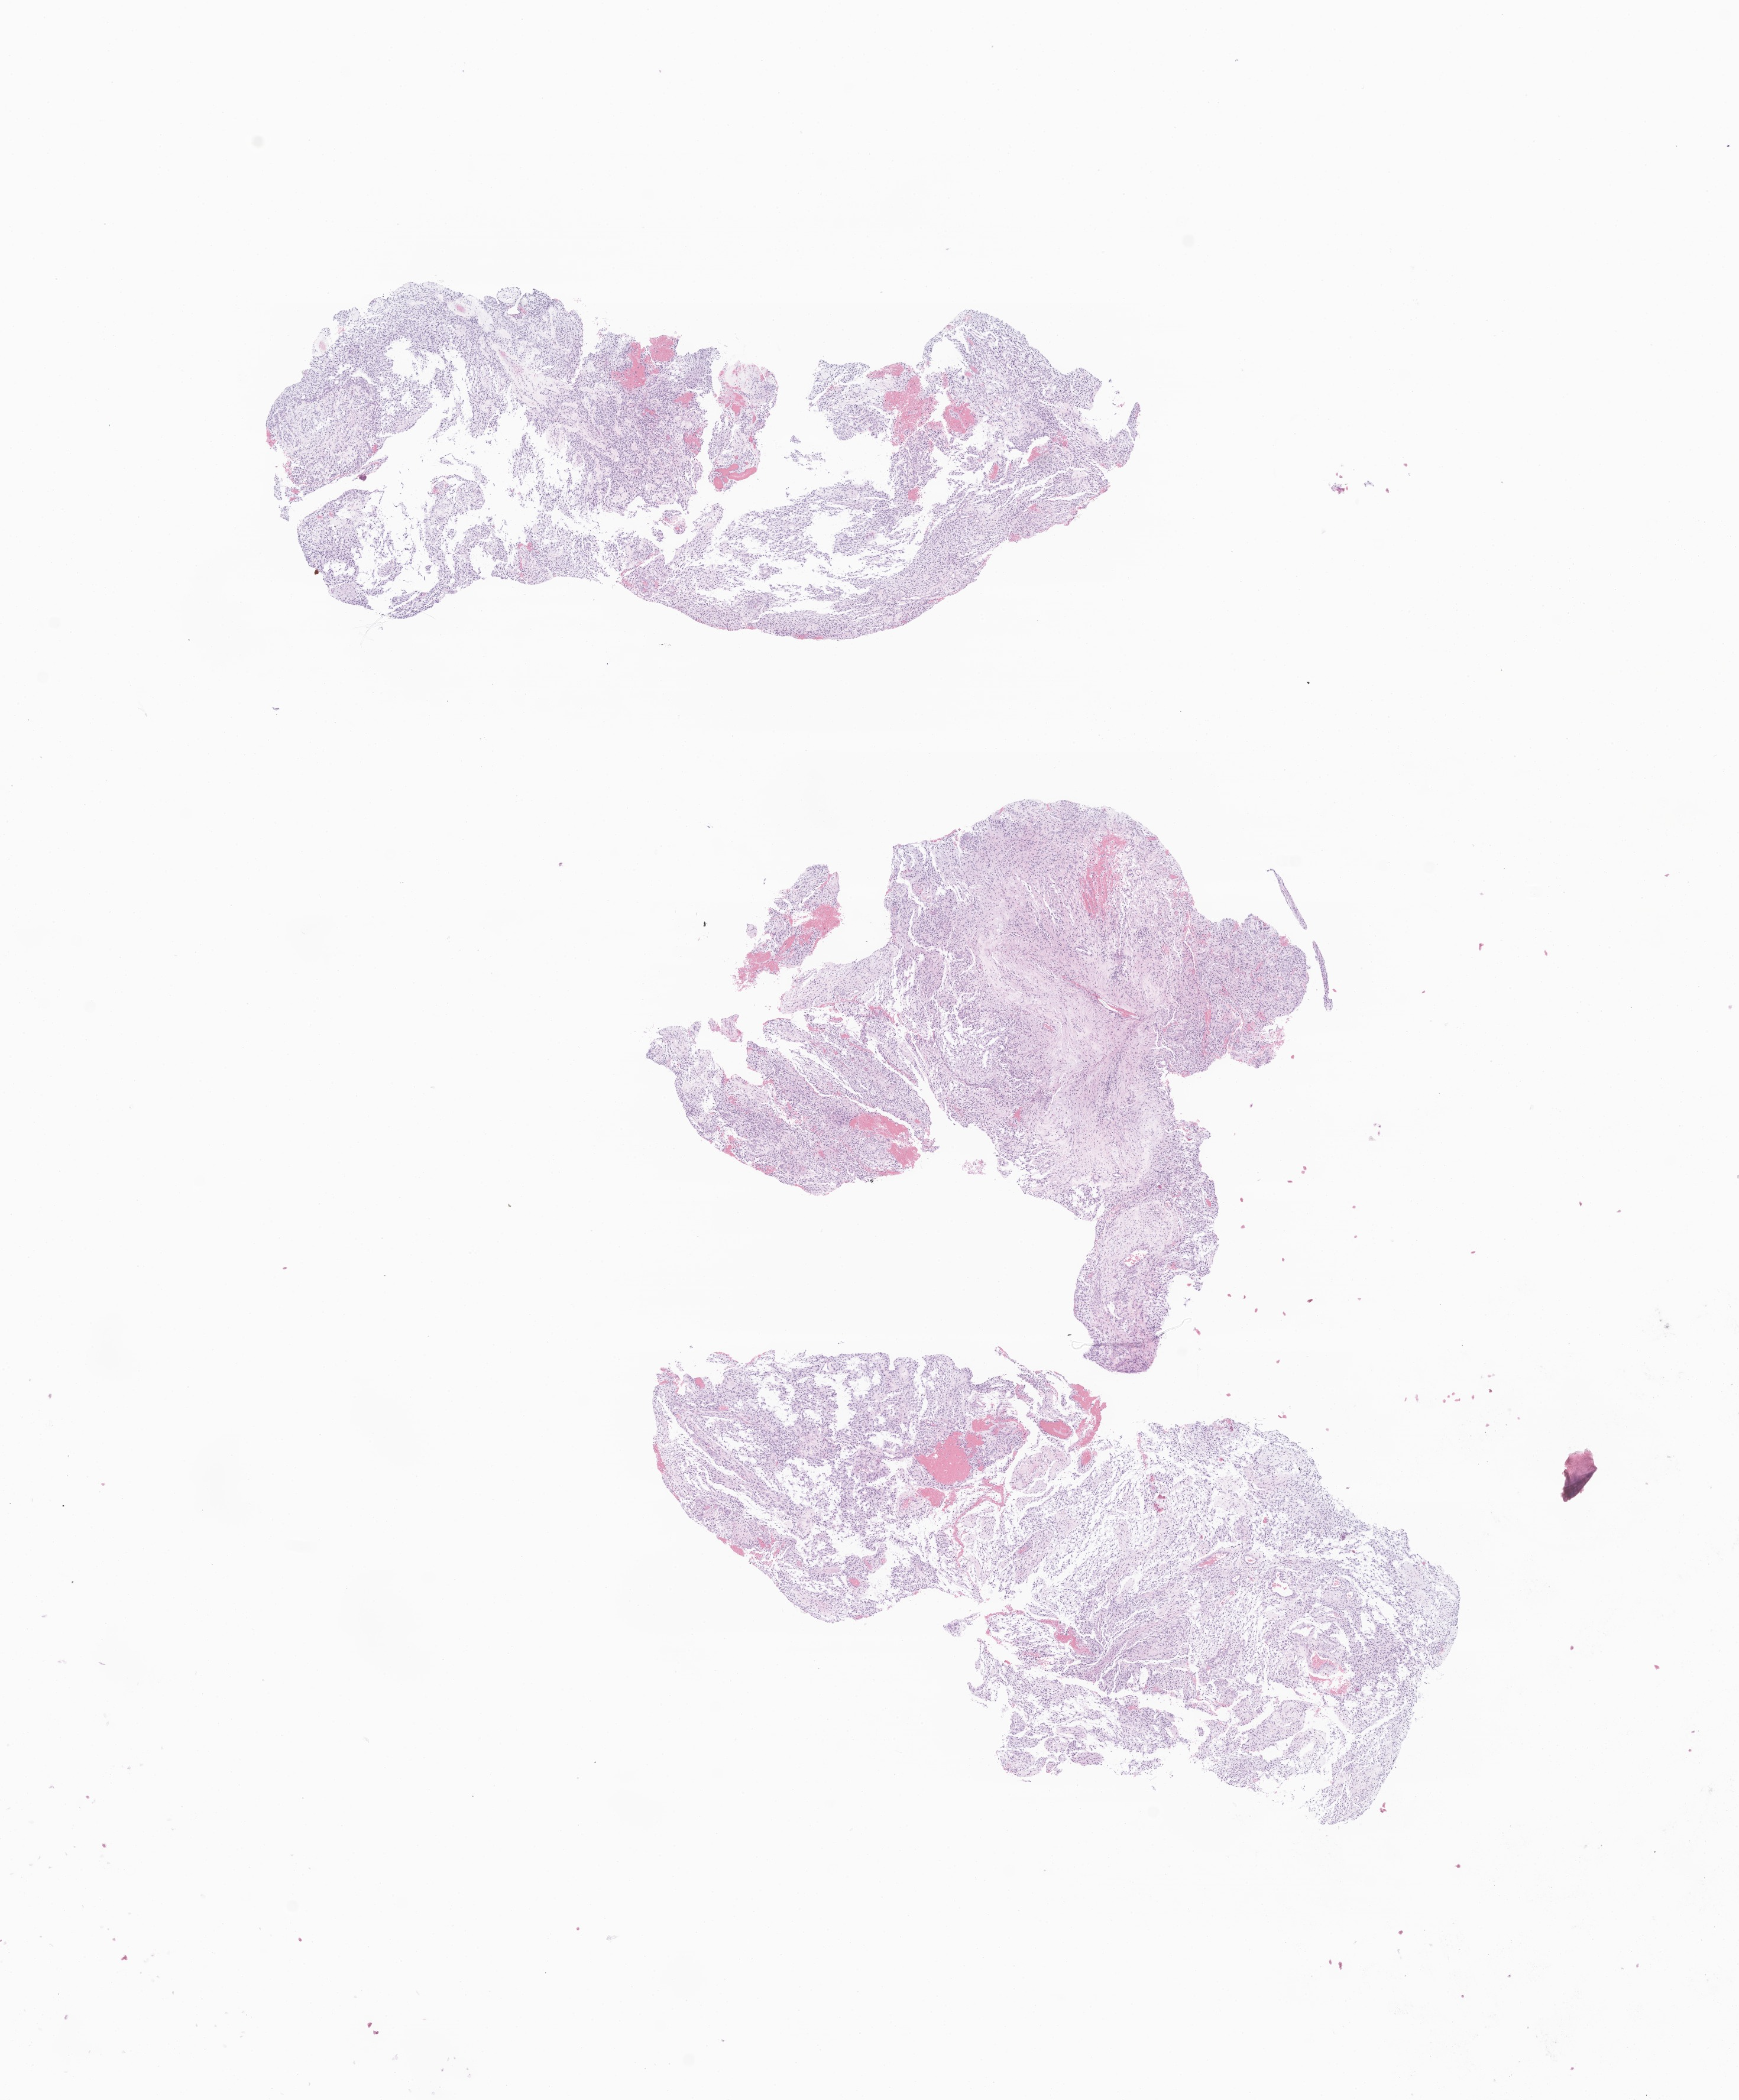
Whole-slide image, haematoxylin and eosin stain of tumor tissue from the brain — shown as a low-resolution overview of the whole scanned area (about 12.4 x 15.0 mm); formalin-fixed, paraffin-embedded (FFPE) tissue. Patient female; age 81 months (6 years 9 months).
* diagnosis: Astrocytoma, NOS